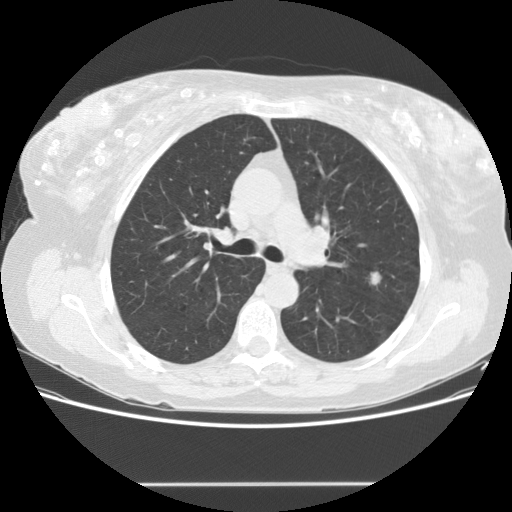
Low-dose screening chest CT, one axial slice. Slice 99 of 151 in the series (ordered by position). 120 kVp. Lung window (W 1500 / L -600 HU). 2.5 mm slice thickness. 512 × 512 image matrix, field of view 360 × 360 mm.
Annotated regions visible in this slice (outlined manually by an expert reader):
- lesion 1 (tumor, upper lobe of left lung): bounding box (x1, y1, x2, y2) in pixels: (370, 272, 381, 285)